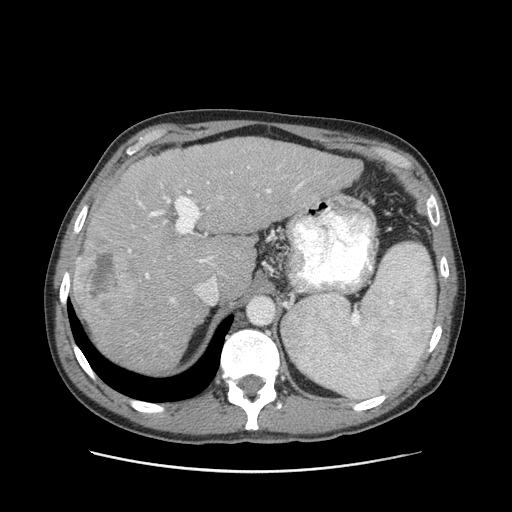
Contrast-enhanced abdominal CT (liver protocol), one axial slice; position 68 of 93 along the scan axis; reconstruction kernel STANDARD; 120 kVp; soft-tissue window (W 400 / L 40 HU); 512 × 512 image matrix, field of view 380 × 380 mm. Case-level facts recorded for this patient, not image findings: diagnosis: hepatocellular carcinoma (patient treated with transarterial chemoembolisation; whether this scan precedes or follows treatment is not stated here); TNM stage (as recorded): Stage-II; Child-Pugh class: A; tumour differentiation: moderately differentiated; tumour nodularity: multinodular.
Annotated regions visible in this slice (semi-automatically segmented with operator editing):
- liver parenchyma outside the tumour (the mass and vessels are separate outlines, so this box may not span the whole liver): bounding box (x1, y1, x2, y2) in pixels: (72, 136, 362, 372)
- mass: (74, 242, 140, 319)
- liver vessels: (79, 166, 303, 302)